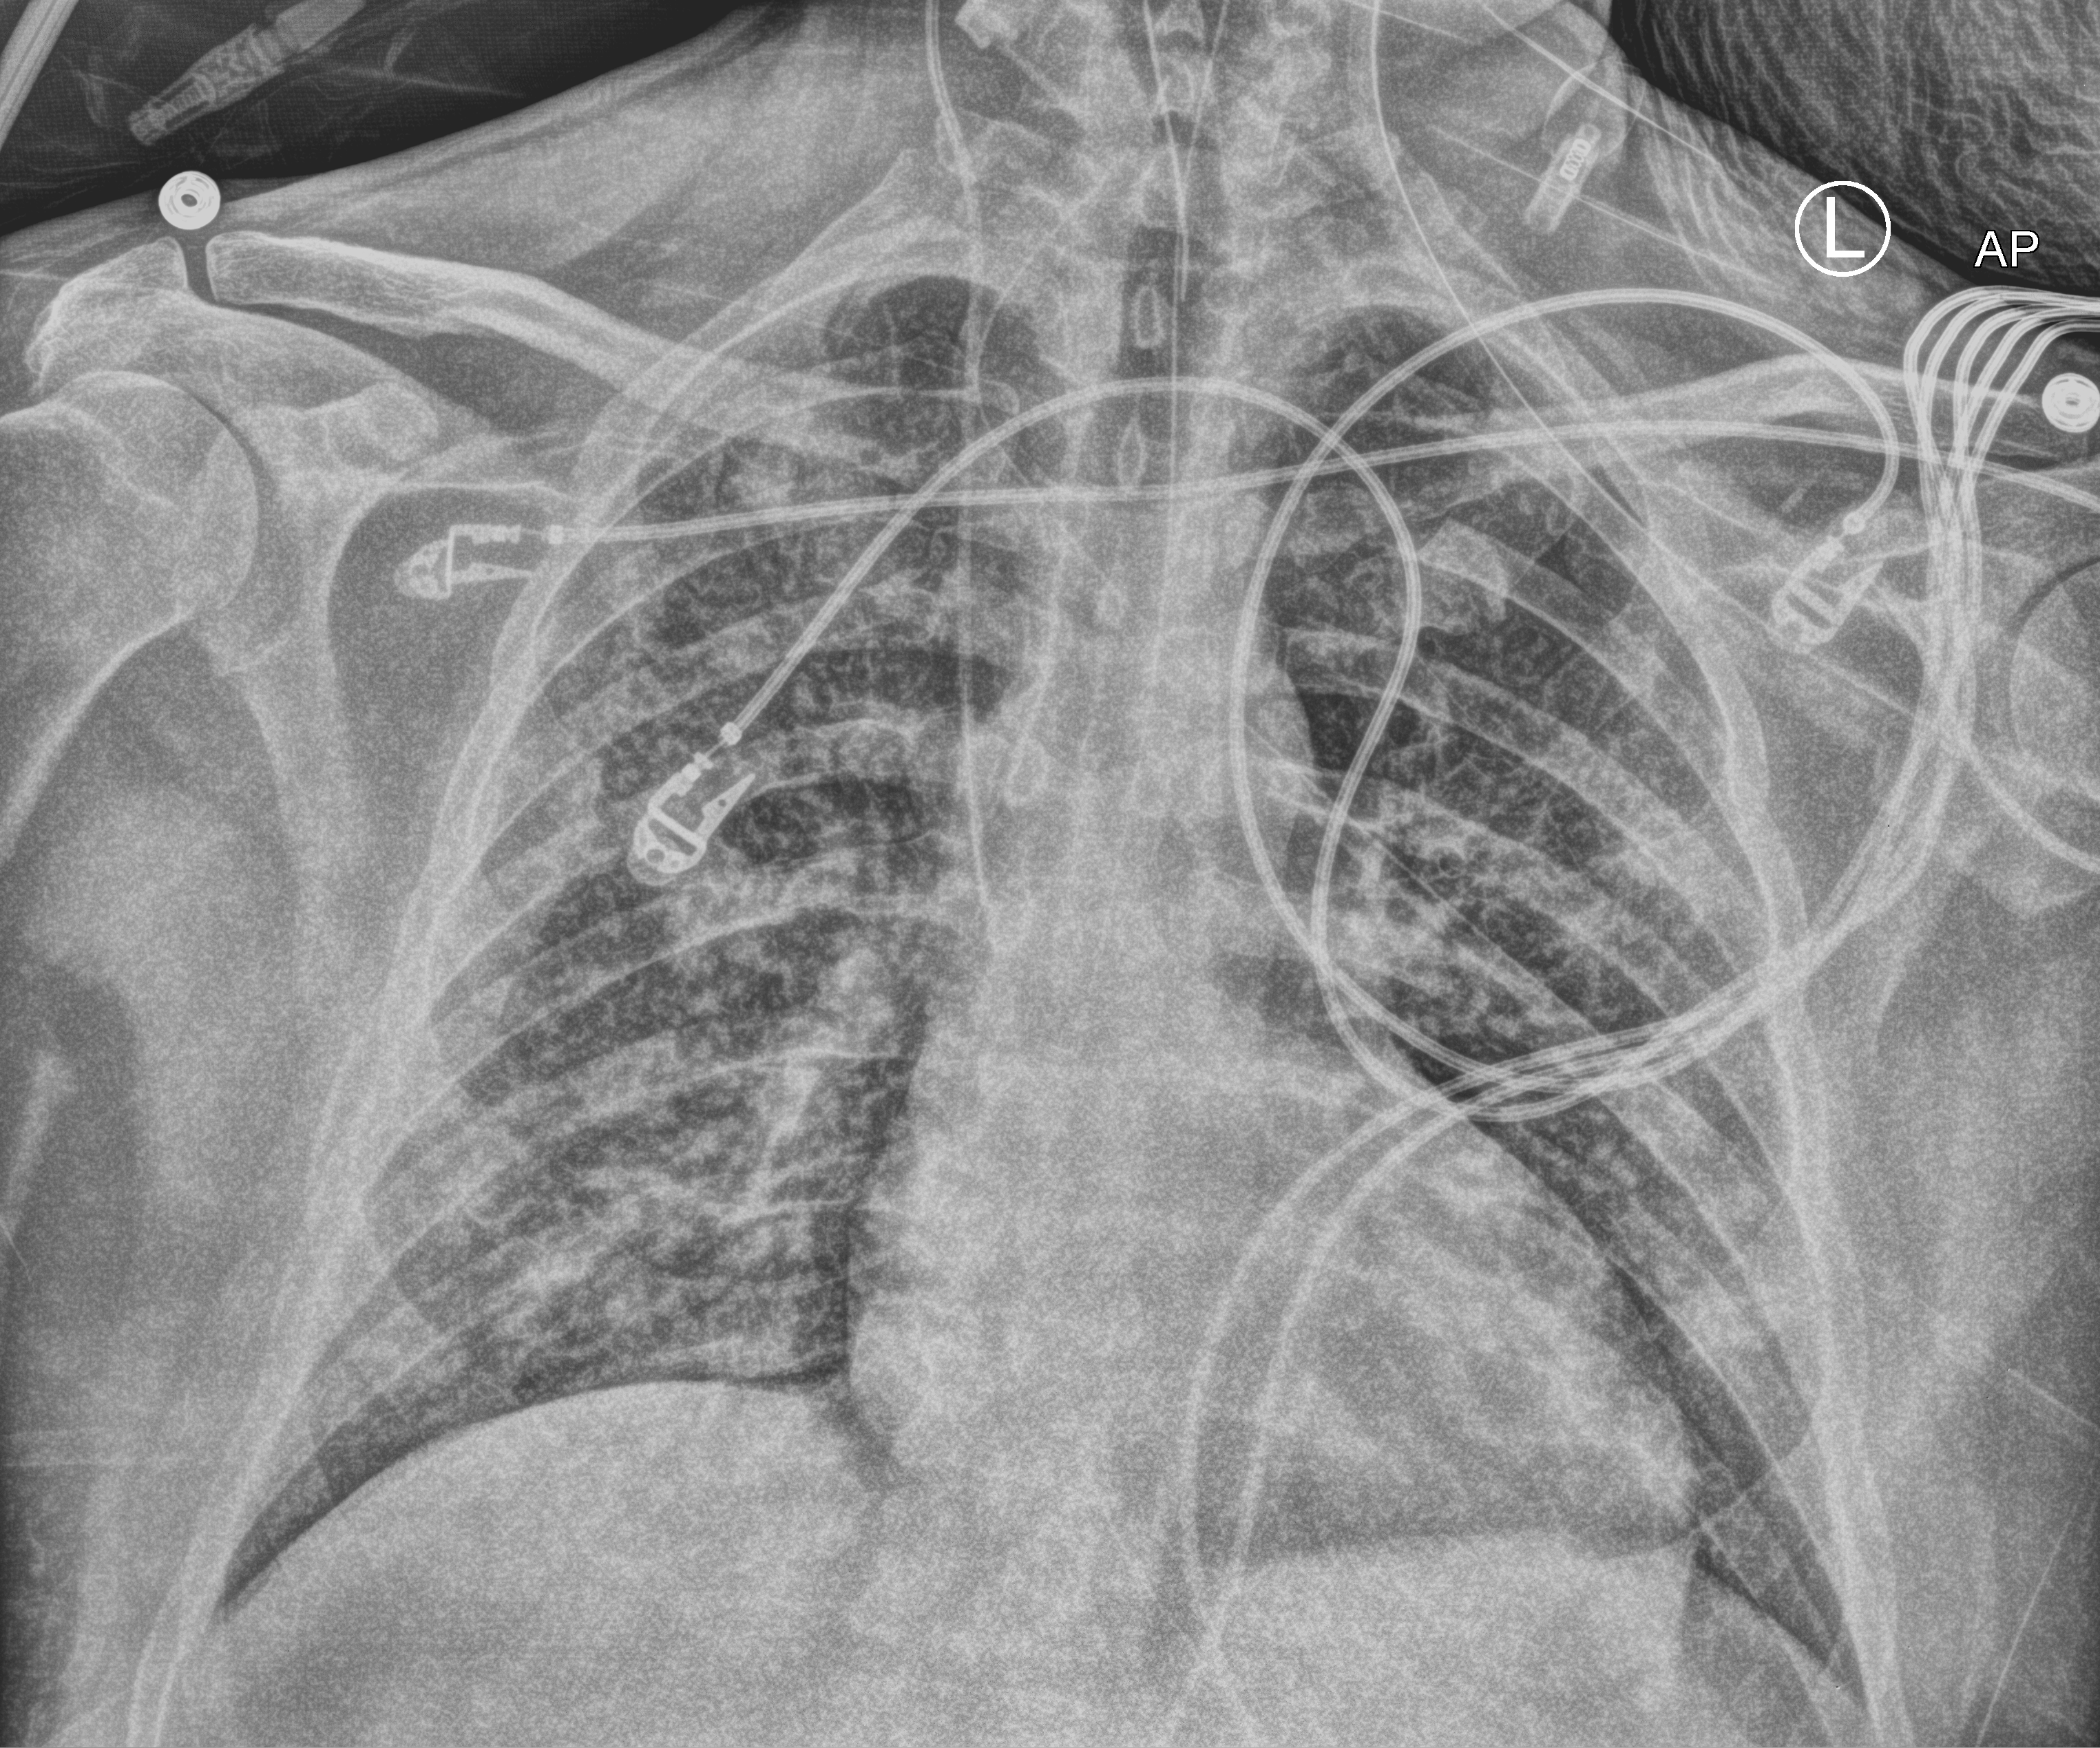
Bedside chest radiograph (computed radiography), anteroposterior (AP) projection. Patient hospitalised with COVID-19; male, aged 18–59 years.
Hospital-stay facts (about this admission, not read from this image; timing relative to this image not recorded): mechanically ventilated during this hospital stay: yes; admitted to intensive care during this hospital stay: no.